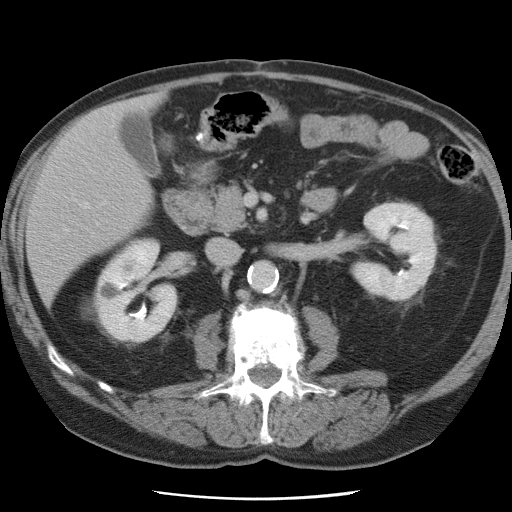
Contrast-enhanced abdominal CT, one axial slice; position 30 of 78 along the scan axis; intravenous contrast given; soft-tissue window (W 400 / L 40 HU); 5 mm slice thickness; 512 × 512 image matrix. Male patient, age 75 years. Case-level facts recorded for this patient, not image findings: diagnosis: colorectal cancer liver metastases, imaged before liver resection.
Annotated regions visible in this slice (expert manual segmentation):
- hepatic veins: box from (x=65, y=204) to (x=88, y=232) px
- liver: (x=29, y=97)–(x=158, y=300)
- planned liver remnant (the part of the liver to remain after resection): (x=29, y=117)–(x=152, y=300)